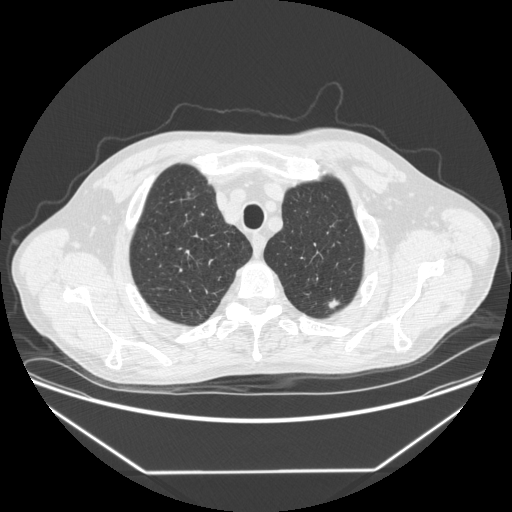
Low-dose screening chest CT, one axial slice; slice 335 of 383 in the series (ordered by position); reconstruction kernel STANDARD; 120 kVp; lung window (W 1500 / L -600 HU); 1.25 mm slice thickness; 512 × 512 image matrix.
Structures marked on this image (outlined manually by an expert reader):
- lesion 1 (tumor, upper lobe of left lung): bounding box (x1, y1, x2, y2) in pixels: (328, 299, 340, 309)